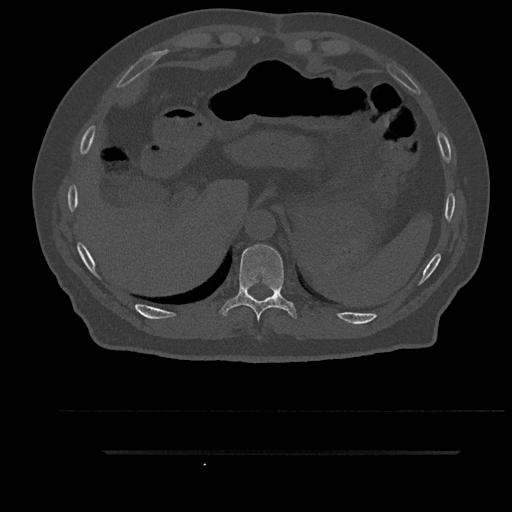
CT including the spine, one axial slice. Position 364 of 797 along the scan axis. Bone window (W 1800 / L 400 HU). 512 × 512 image matrix. Patient: male, 63 years. From the clinical record (not read from this slice): primary cancer: renal; vertebrae with lytic lesions (as recorded): T8.
Annotated regions visible in this slice (semi-automatically segmented with operator editing):
- T10 vertebra: bounding box (x1, y1, x2, y2) in pixels: (219, 244, 297, 321)